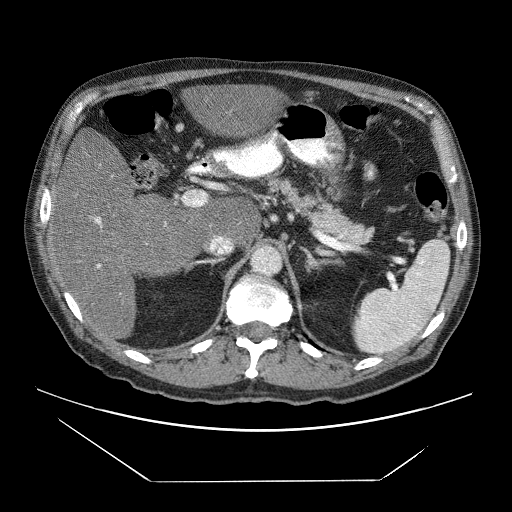
Contrast-enhanced abdominal CT (liver protocol), one axial slice; reconstruction kernel STANDARD; 120 kVp; soft-tissue window (W 400 / L 40 HU); 2.5 mm slice thickness; 512 × 512 image matrix. From the clinical record (not read from this slice): diagnosis: hepatocellular carcinoma (patient treated with transarterial chemoembolisation; whether this scan precedes or follows treatment is not stated here); TNM stage (as recorded): Stage-IVB; Child-Pugh class: B; tumour differentiation: poorly differentiated.
Outlined on this slice (semi-automatically segmented with operator editing):
- liver parenchyma outside the tumour (the mass and vessels are separate outlines, so this box may not span the whole liver): bounding box (x1, y1, x2, y2) in pixels: (48, 83, 276, 340)
- liver vessels: (94, 217, 167, 268)